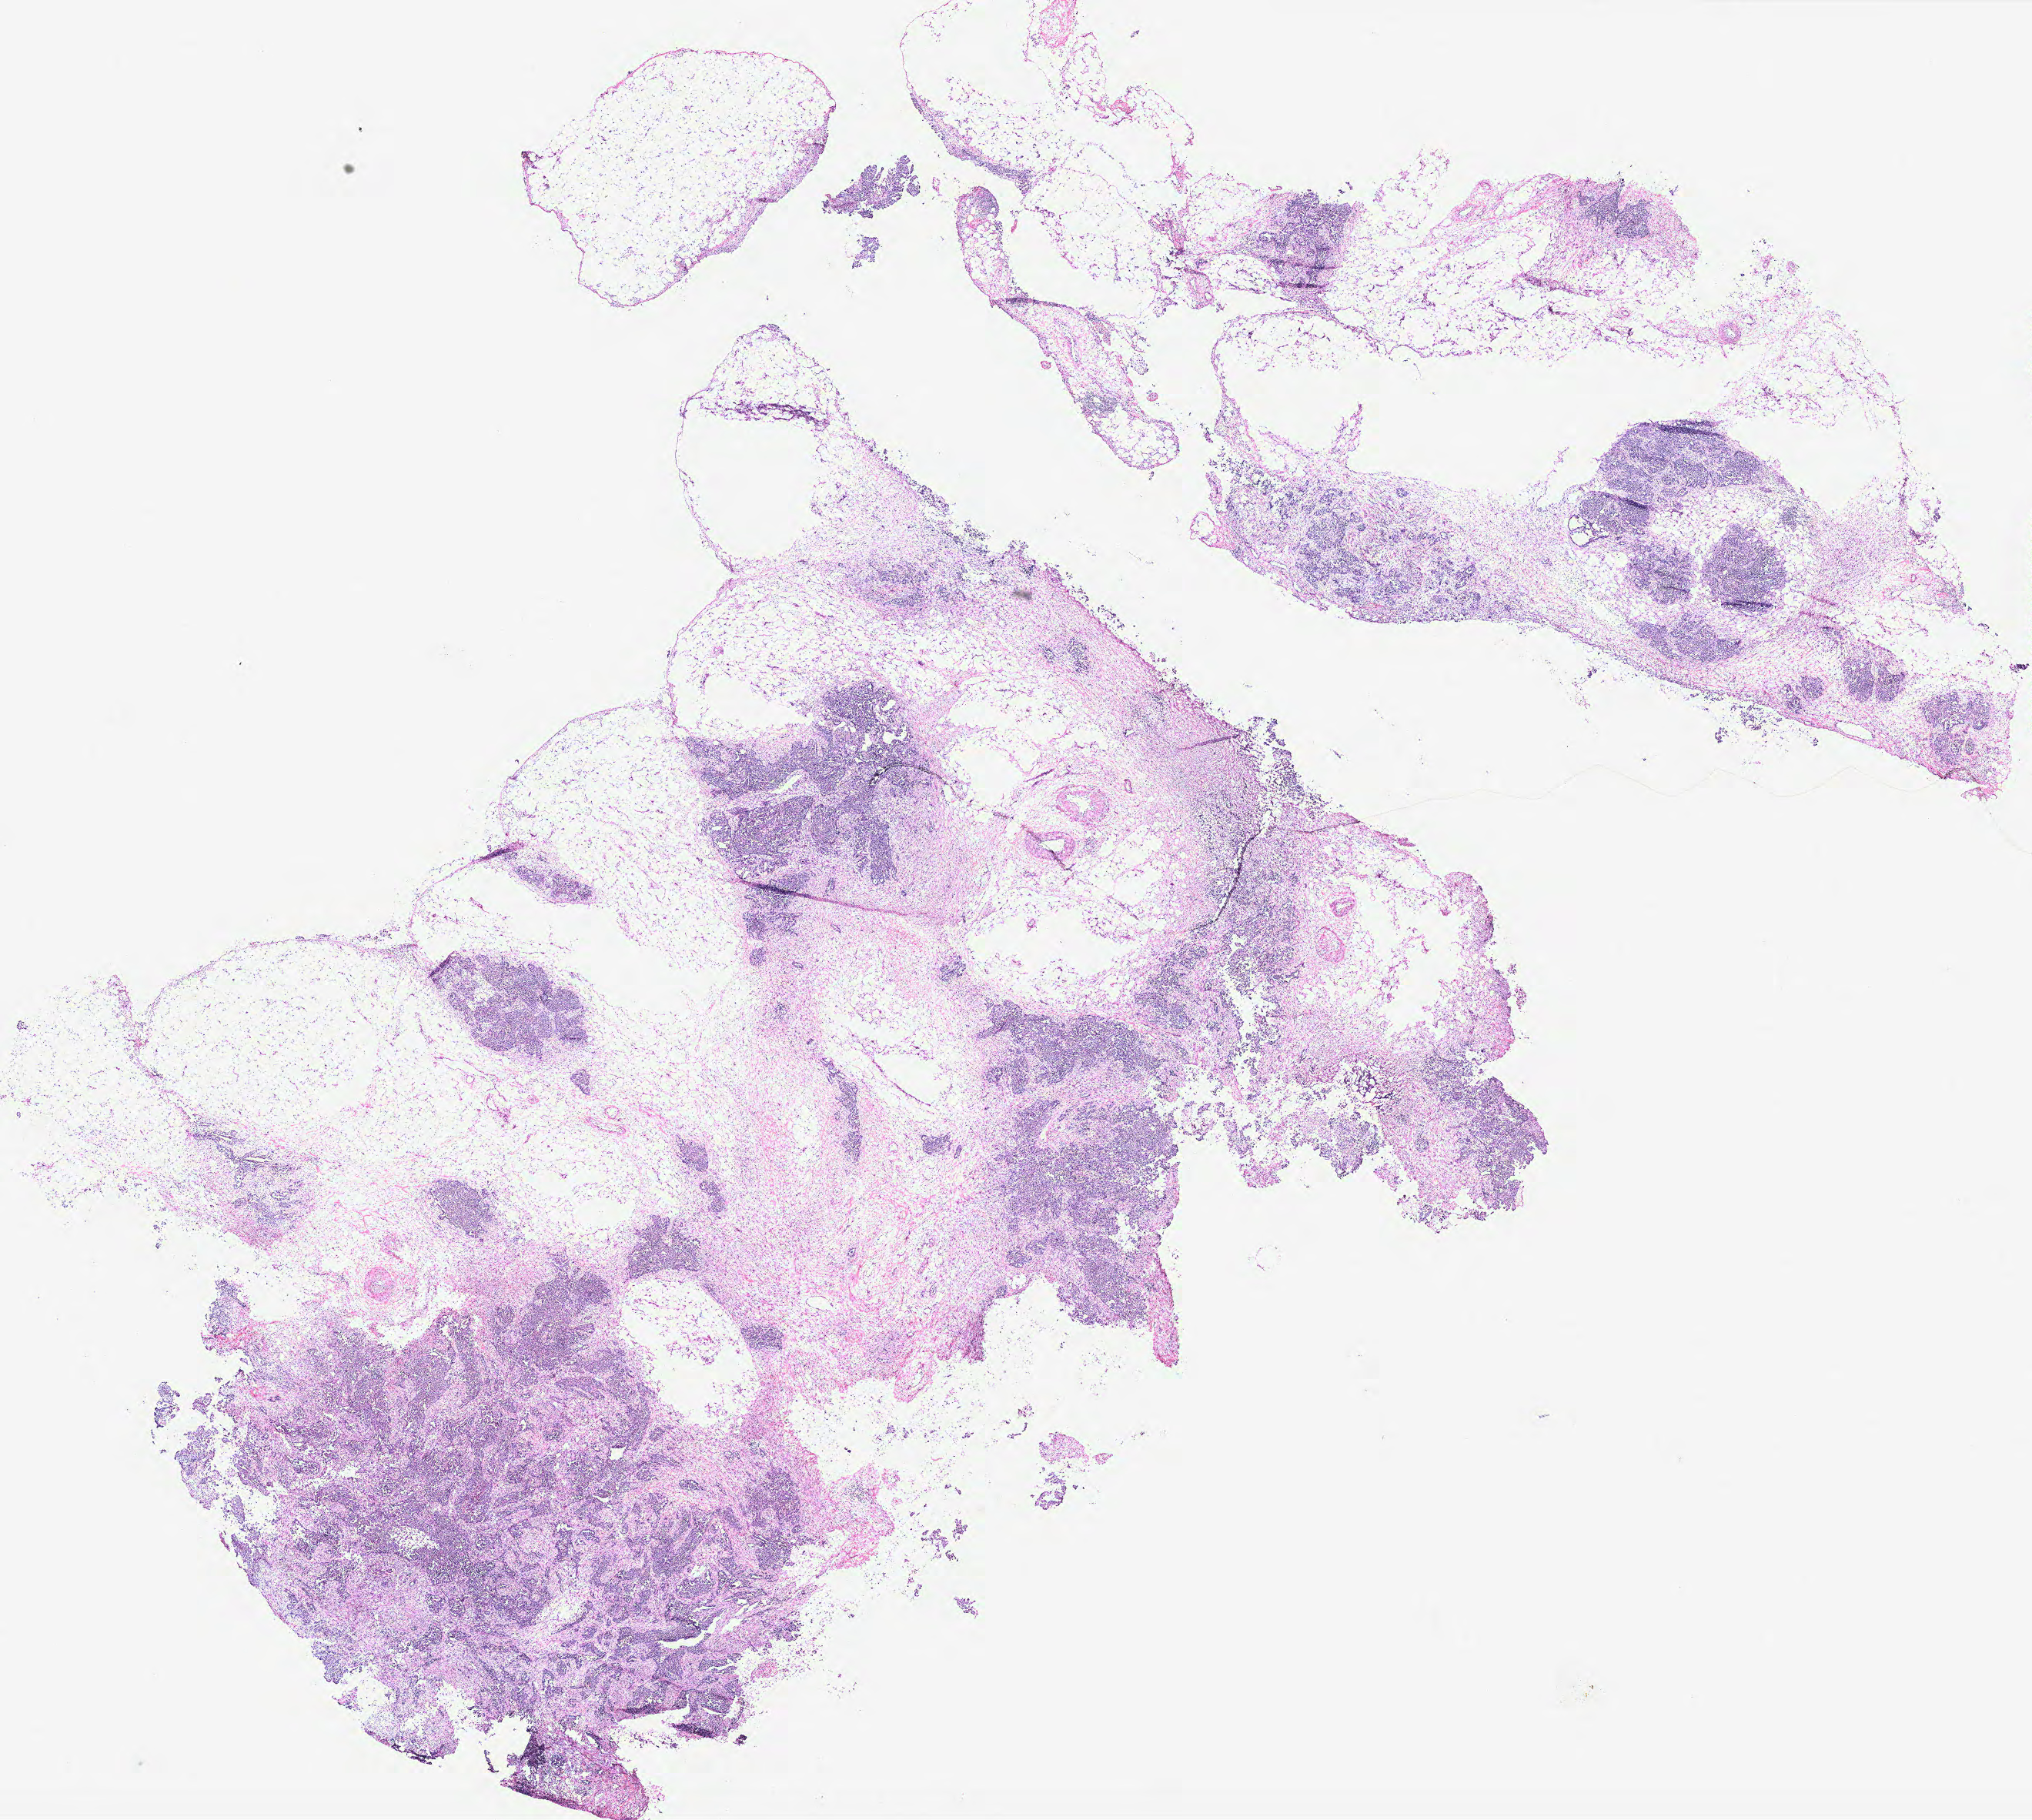
Hematoxylin and eosin (H&E) stained whole-slide image — a low-resolution overview of the entire scanned area, about 21.1 x 18.9 mm (acquisition: 40x scan), ovary, tissue type not recorded. Patient sex: female.
Patient diagnosis: Serous adenocarcinoma, NOS.